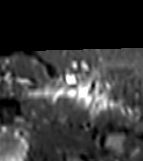
MRI of an extremity soft-tissue mass, one axial slice. Position 54 of 81 along the scan axis. STIR. MR volume resampled by the dataset authors to the PET/CT grid (not the native acquisition matrix). 3.27 mm slice thickness. 143 × 161 image matrix, field of view 140 × 157 mm. Female patient. Case-level facts recorded for this patient, not image findings: histological type: myxofibrosarcoma; grade: intermediate; site of the primary tumour: left thigh.
Outlined on this slice (expert contour drawn on MRI and transferred to this co-registered scan by the dataset authors):
- gross tumour volume including surrounding oedema: bounding box <29,78,114,107> (left, top, right, bottom; pixels)